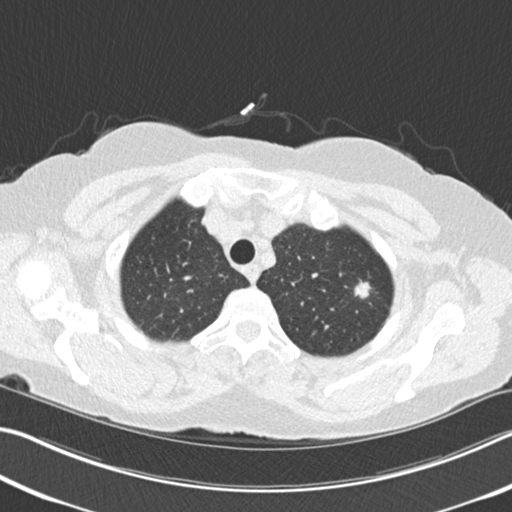
Chest CT (low-dose screening protocol), one axial image; second screening round (one year after baseline); lung window (W 1500 / L -600 HU); 2 mm slice thickness; standard (soft-tissue) reconstruction kernel (B30f). Female participant, aged 64 years at enrolment.
Expert reader's lesion annotation, bounding box <344,272,377,304> (left, top, right, bottom; pixels). The exam's reader record, not a measurement of the box and not confirmed to be the same lesion: non-calcified nodule or mass ≥4 mm, left upper lobe, 13 × 10 mm, spiculated (stellate) margins, soft tissue attenuation, pre-existing on the prior screen: yes; interval growth: yes. Official screen result: positive, other. Lung cancer was diagnosed 106 days after this screen: signet ring cell carcinoma, right upper lobe, poorly differentiated (G3), stage IA (AJCC 6th edition), 15 mm at pathology.